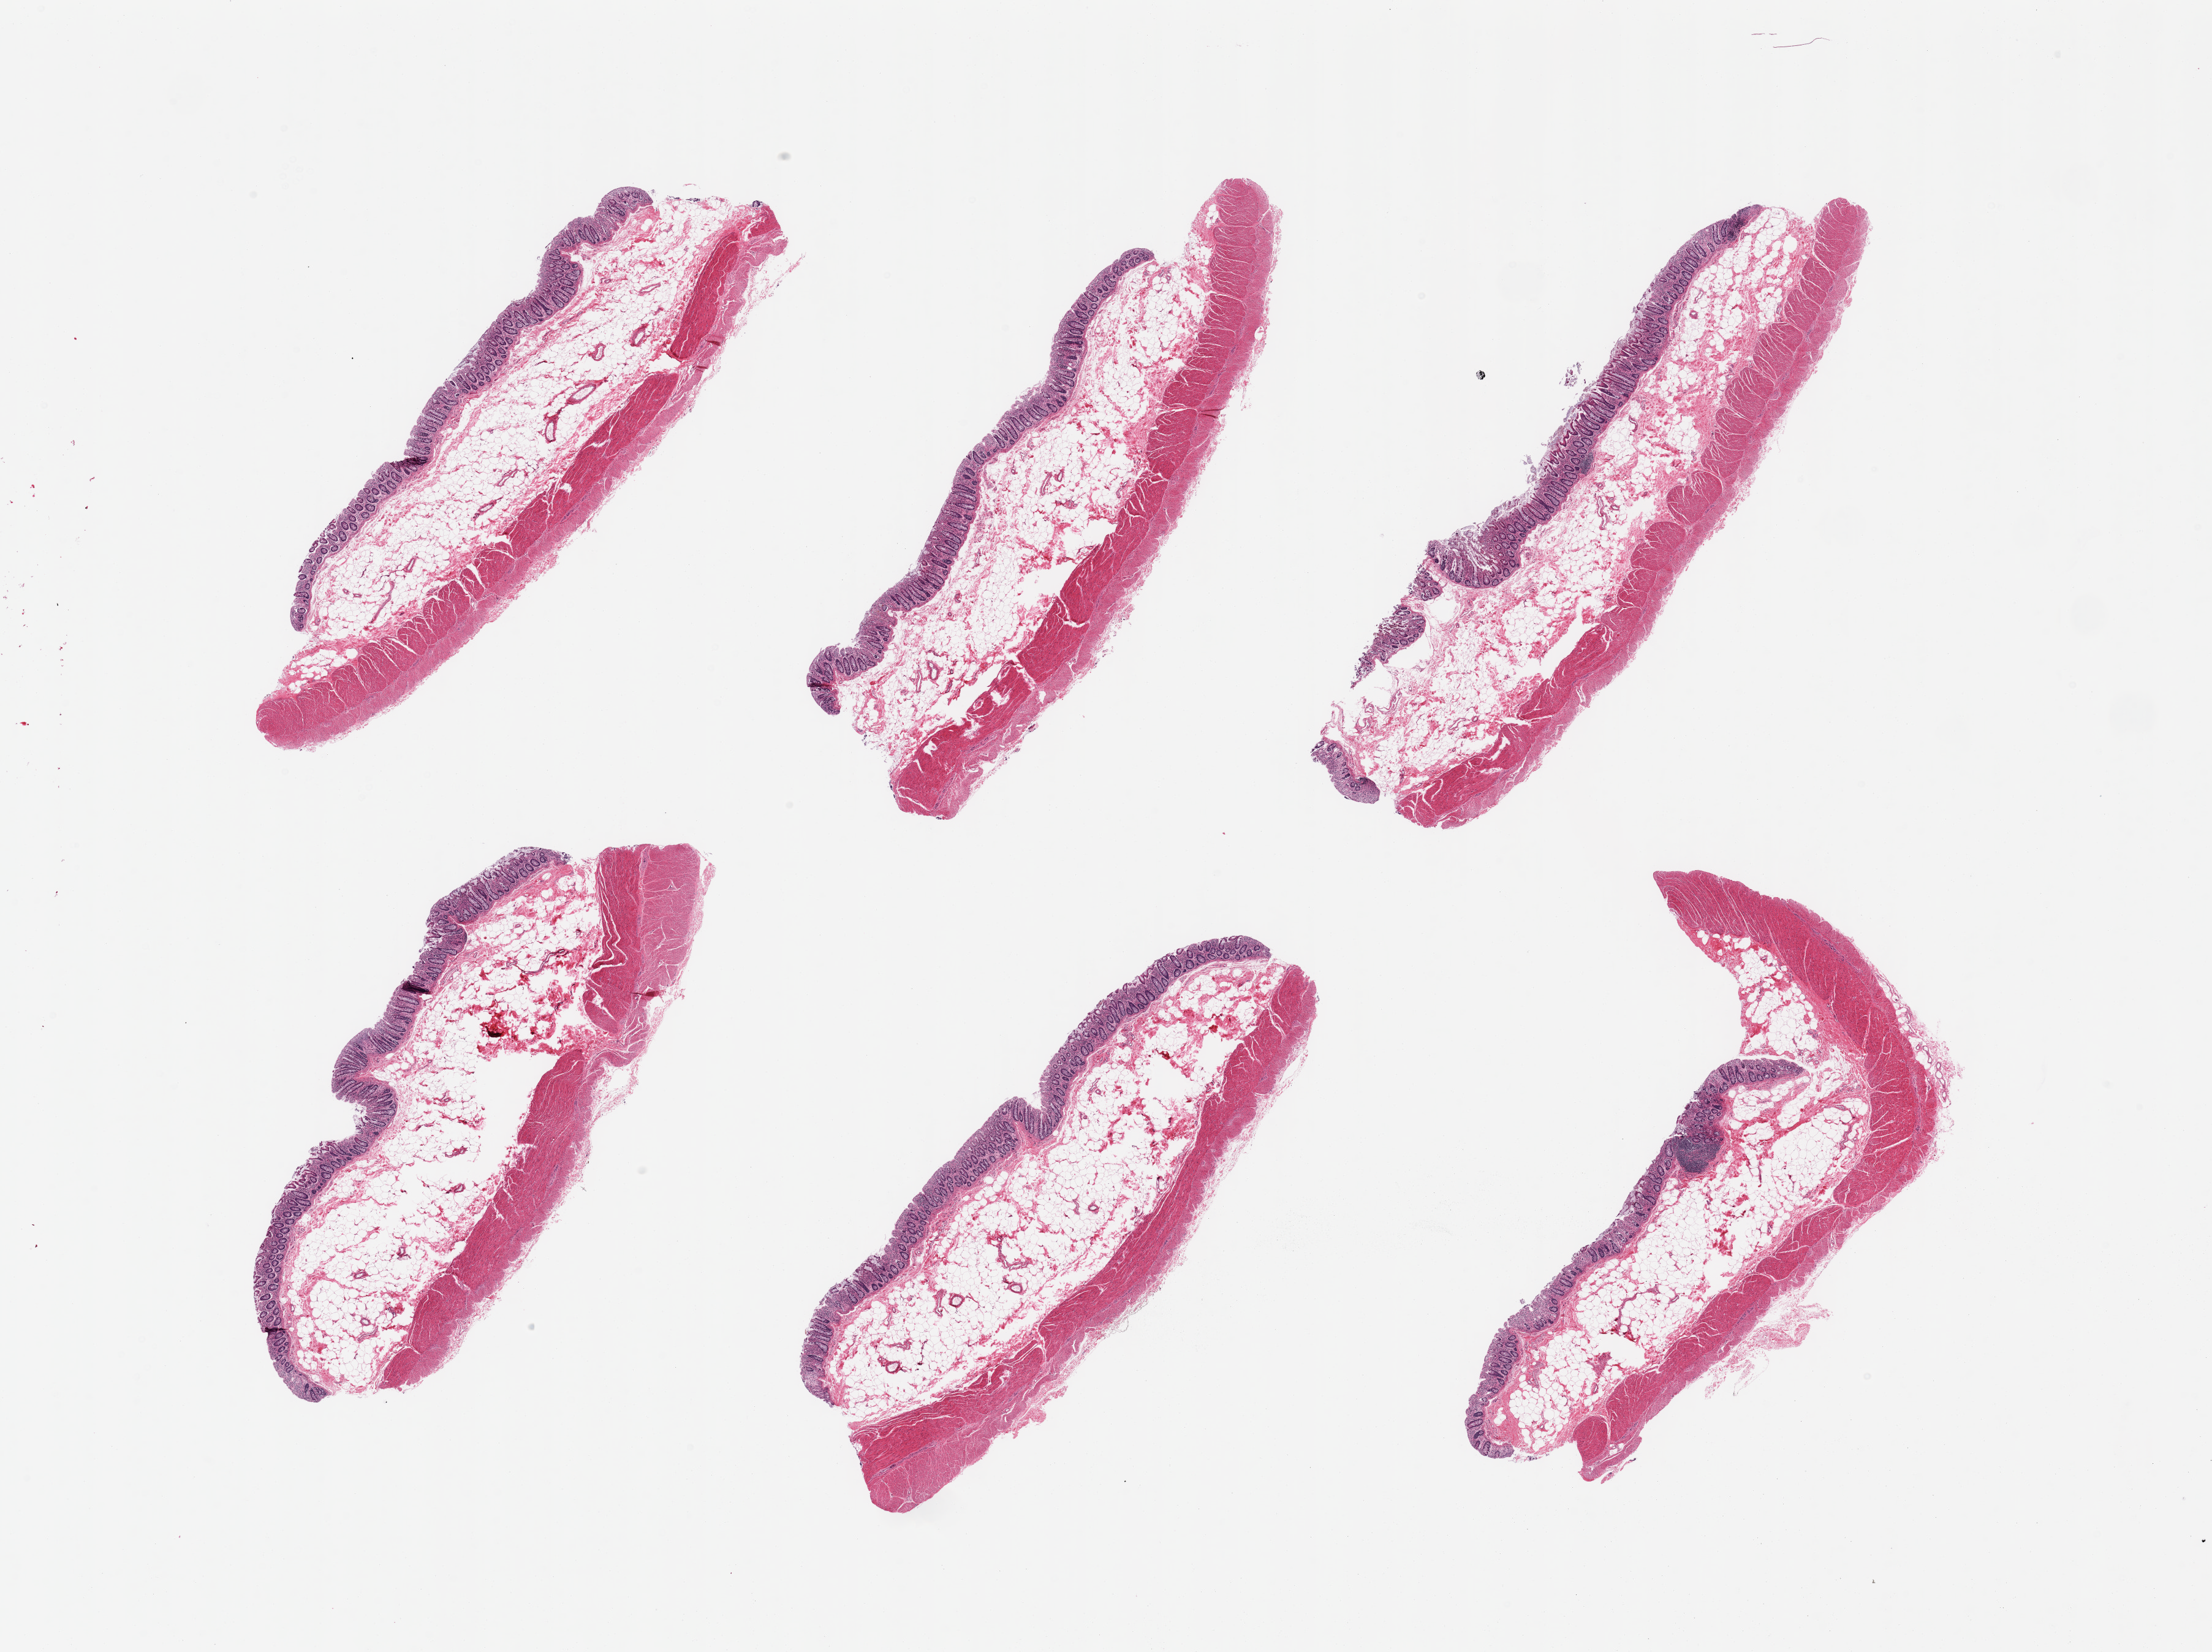
Digitized hematoxylin and eosin (H&E)-stained section — shown as a low-resolution overview of the whole scanned area (about 28.5 x 21.3 mm); PAXgene-fixed paraffin-embedded (PFPE) section; section of transverse colon (target tissue); tissue donor sample. Donor: male.
Pathologist's review note for this sample: 6 pieces, target mucosa with moderately advanced autolysis, up to ~0.4mm, ~10-20% thickness.